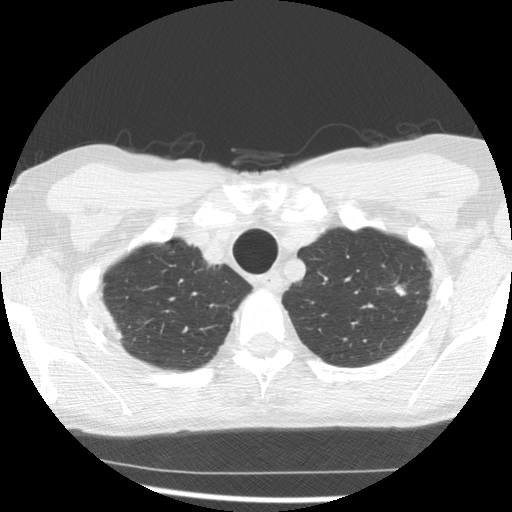
Low-dose screening chest CT, one axial slice. 140 kVp. Lung window (W 1500 / L -600 HU). 2.5 mm slice thickness. 512 × 512 image matrix, field of view 320 × 320 mm.
Annotated regions visible in this slice (manually delineated by an expert):
- lesion 2 (nodule, upper lobe of left lung): bounding box [x1, y1, x2, y2] px = [394, 285, 406, 296]